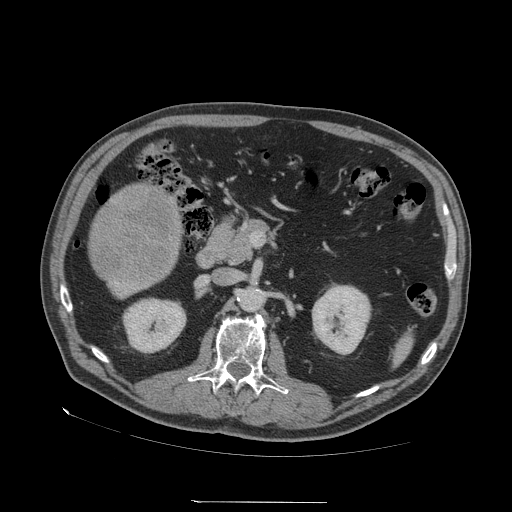
Contrast-enhanced abdominal CT (liver protocol), one axial slice. Position 11 of 83 along the scan axis. 140 kVp. Soft-tissue window (W 400 / L 40 HU). 2.5 mm slice thickness. 512 × 512 image matrix. Case-level facts recorded for this patient, not image findings: diagnosis: hepatocellular carcinoma (patient treated with transarterial chemoembolisation; whether this scan precedes or follows treatment is not stated here); TNM stage (as recorded): Stage-I; Child-Pugh class: A.
Structures marked on this image (semi-automatically segmented with operator editing):
- liver parenchyma outside the tumour (the mass and vessels are separate outlines, so this box may not span the whole liver): bounding box (x1, y1, x2, y2) in pixels: (110, 279, 128, 296)
- mass: (92, 187, 182, 281)